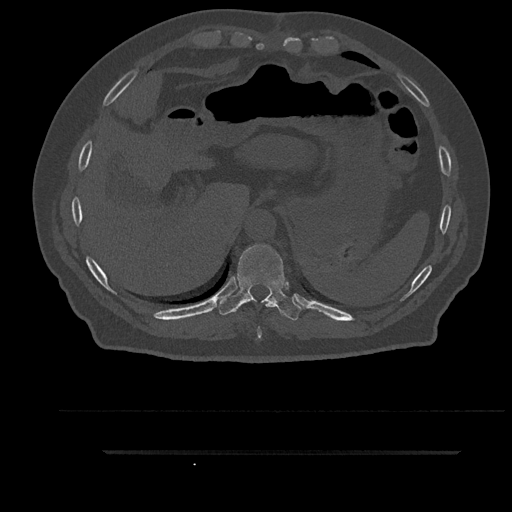
CT including the spine, one axial slice. Slice 381 of 797 in the series (ordered by position). Reconstruction kernel Br40s/3. 120 kVp. Bone window (W 1800 / L 400 HU). 0.5 mm slice thickness. 512 × 512 image matrix. Patient: male, 63 years. Case-level facts recorded for this patient, not image findings: primary cancer: renal.
Structures marked on this image (semi-automatically segmented with operator editing):
- T10 vertebra: bounding box (x1, y1, x2, y2) in pixels: (218, 245, 303, 321)
- T9 vertebra: (257, 301, 272, 339)